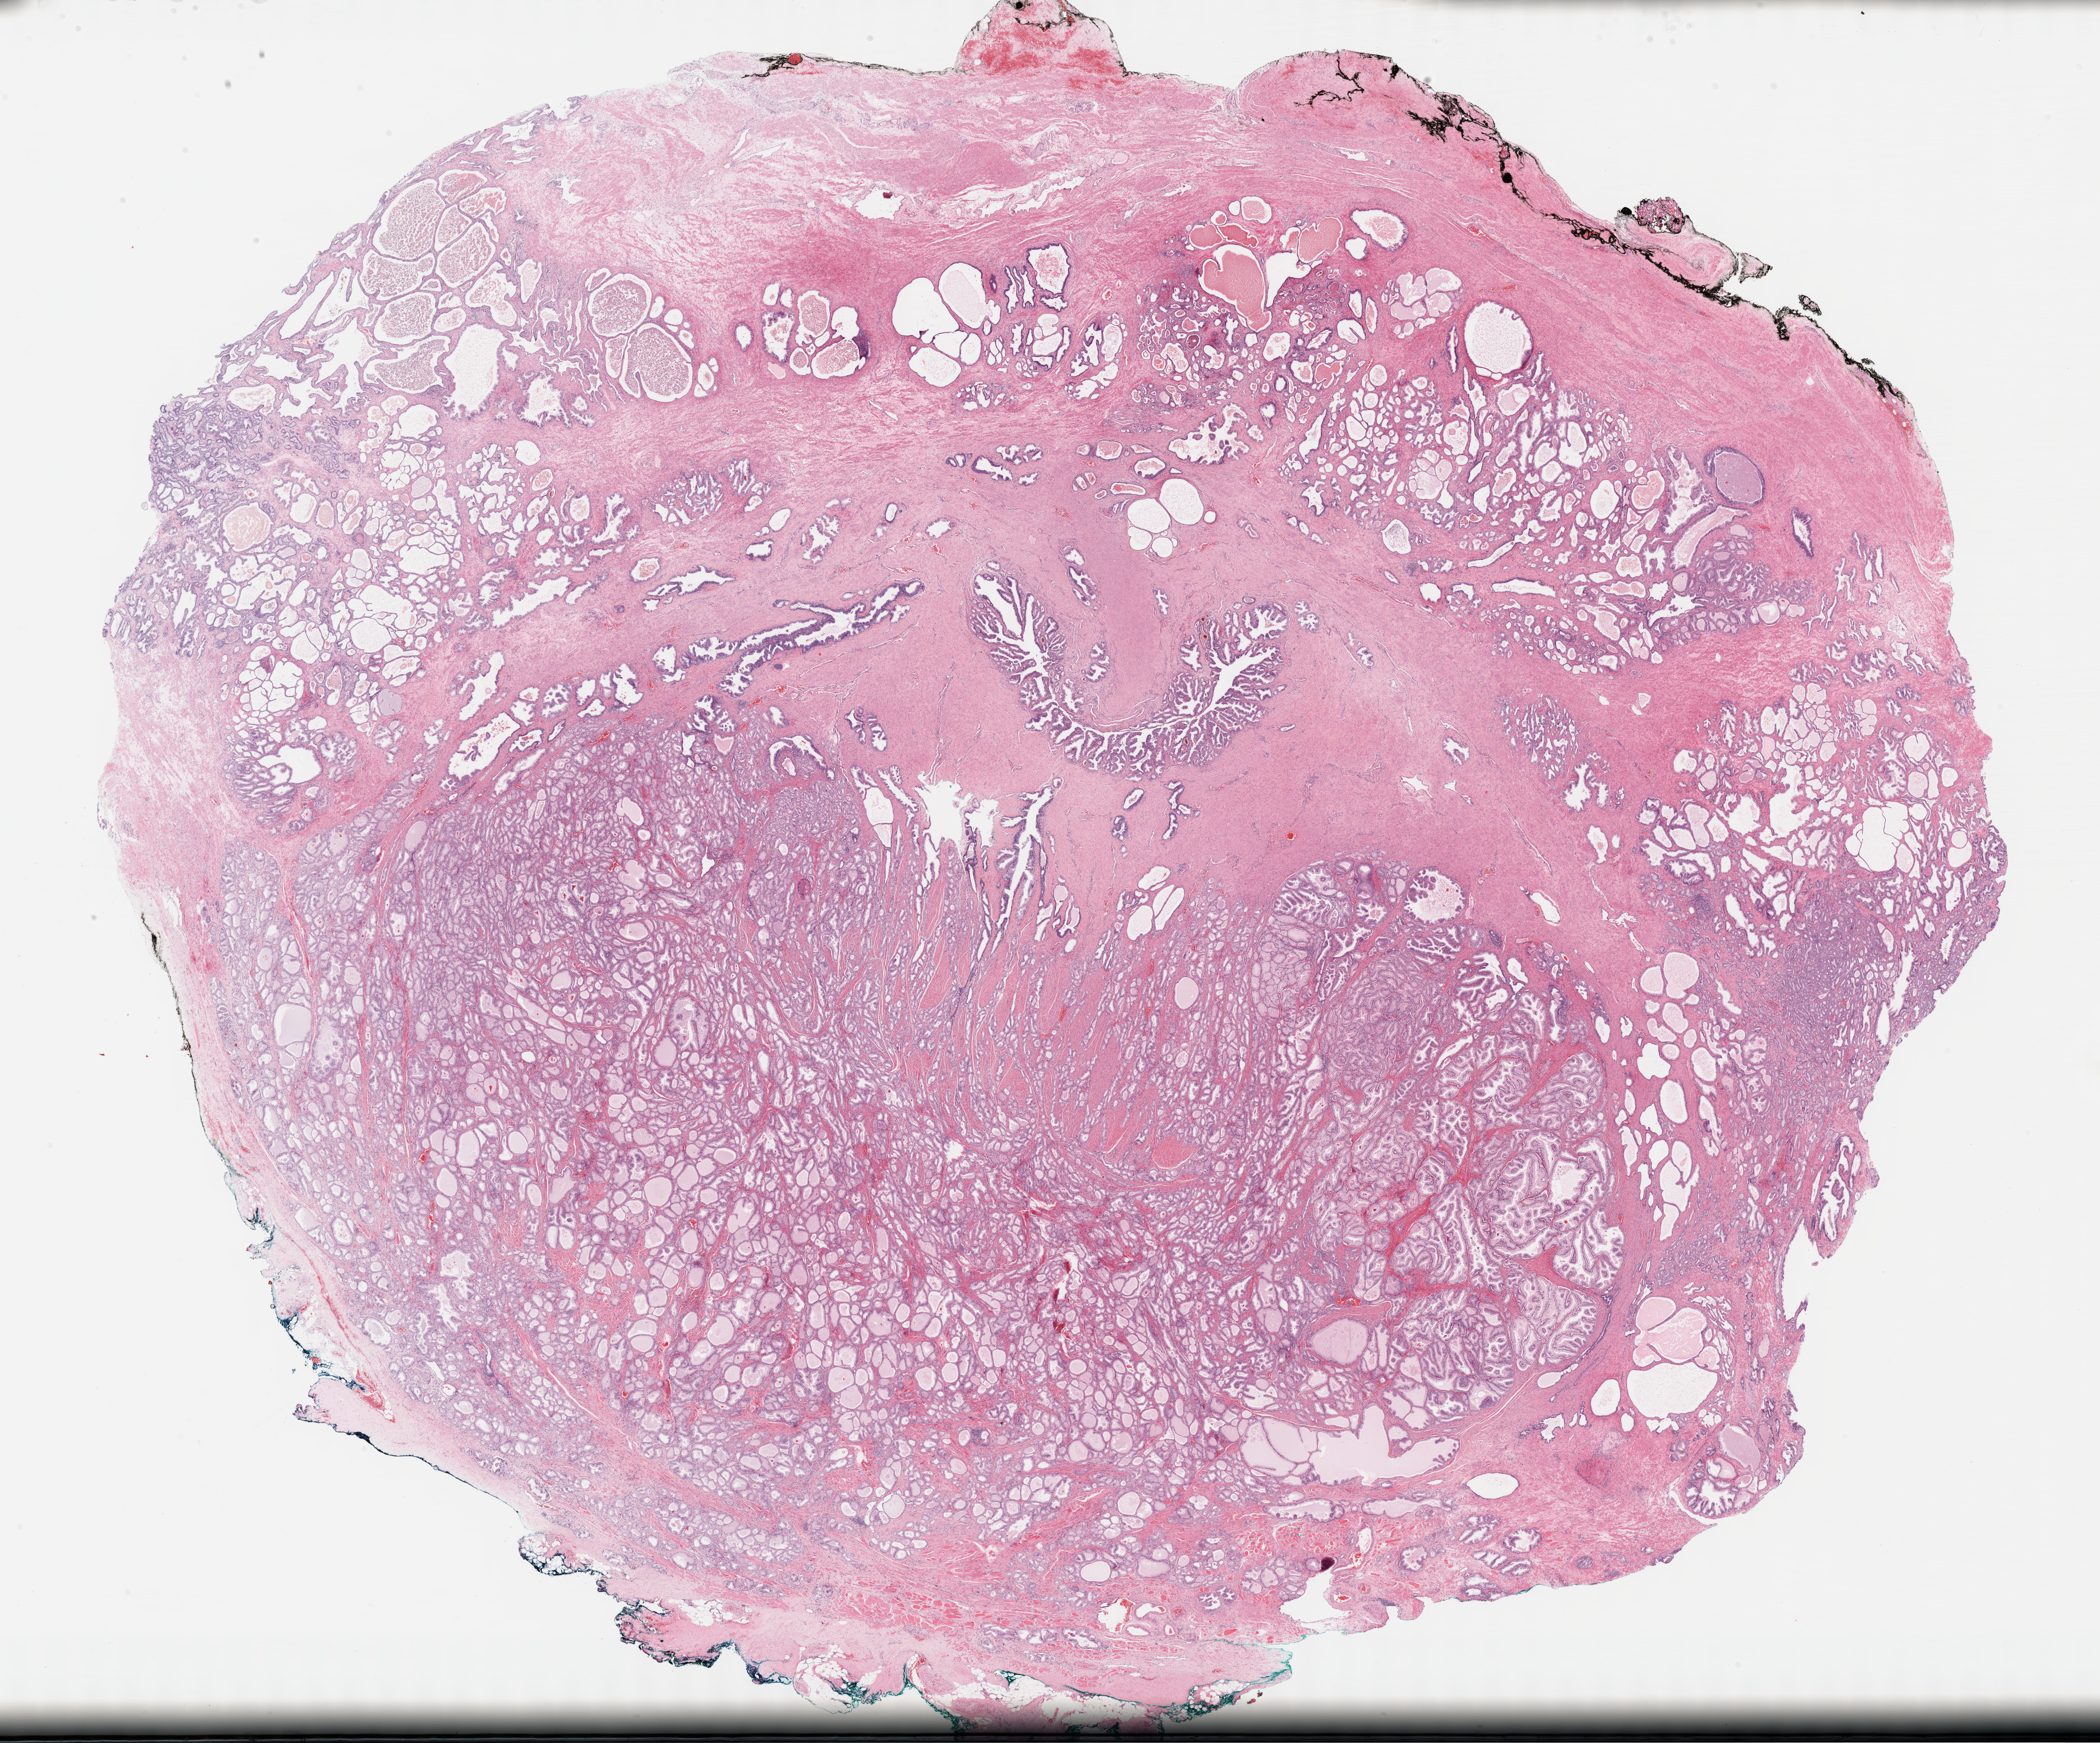
Digitized H&E-stained tissue section (whole slide) — low-resolution overview of the scanned area, about 28.7 x 23.8 mm (slide scanned at 40x); FFPE section; sample: primary tumour, prostate. Patient: male, age at initial diagnosis 67 years. Gleason score: 6 (3+3).
Diagnosis: Adenocarcinoma, NOS (prostate gland).